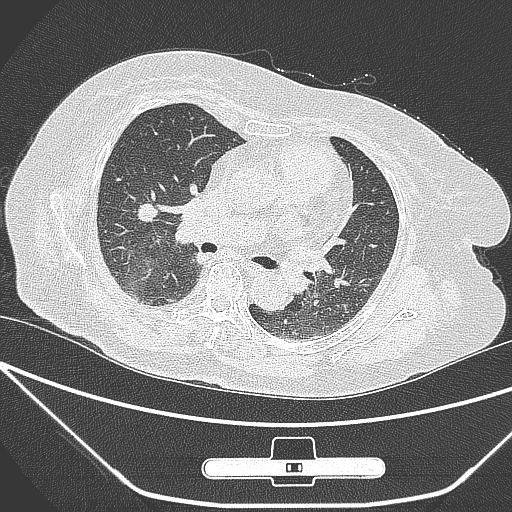
Chest CT, one axial slice. Position 155 of 245 along the scan axis. 120 kVp. Lung window (W 1500 / L -600 HU). 1 mm slice thickness. 512 × 512 image matrix, field of view 365 × 365 mm. Female patient, age 65 years. From the clinical record (not read from this slice): clinical TNM (as recorded): T1c N0 M0; histopathological grade: G3.
Structures marked on this image (bounding box drawn by a radiologist):
- lung tumour (recorded histology: adenocarcinoma): box from (x=132, y=198) to (x=164, y=233) px